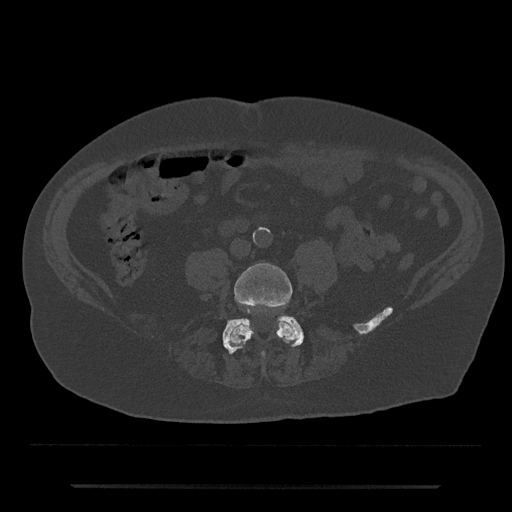
CT including the spine, one axial slice. Position 325 of 797 along the scan axis. Reconstruction kernel Br40s/3. Bone window (W 1800 / L 400 HU). 0.5 mm slice thickness. 512 × 512 image matrix. Patient: male, 80 years. Case-level facts recorded for this patient, not image findings: primary cancer: prostate.
Structures marked on this image (semi-automatically segmented with operator editing):
- L4 vertebra: bounding box <228,263,297,357> (left, top, right, bottom; pixels)
- L5 vertebra: <222,316,304,354>